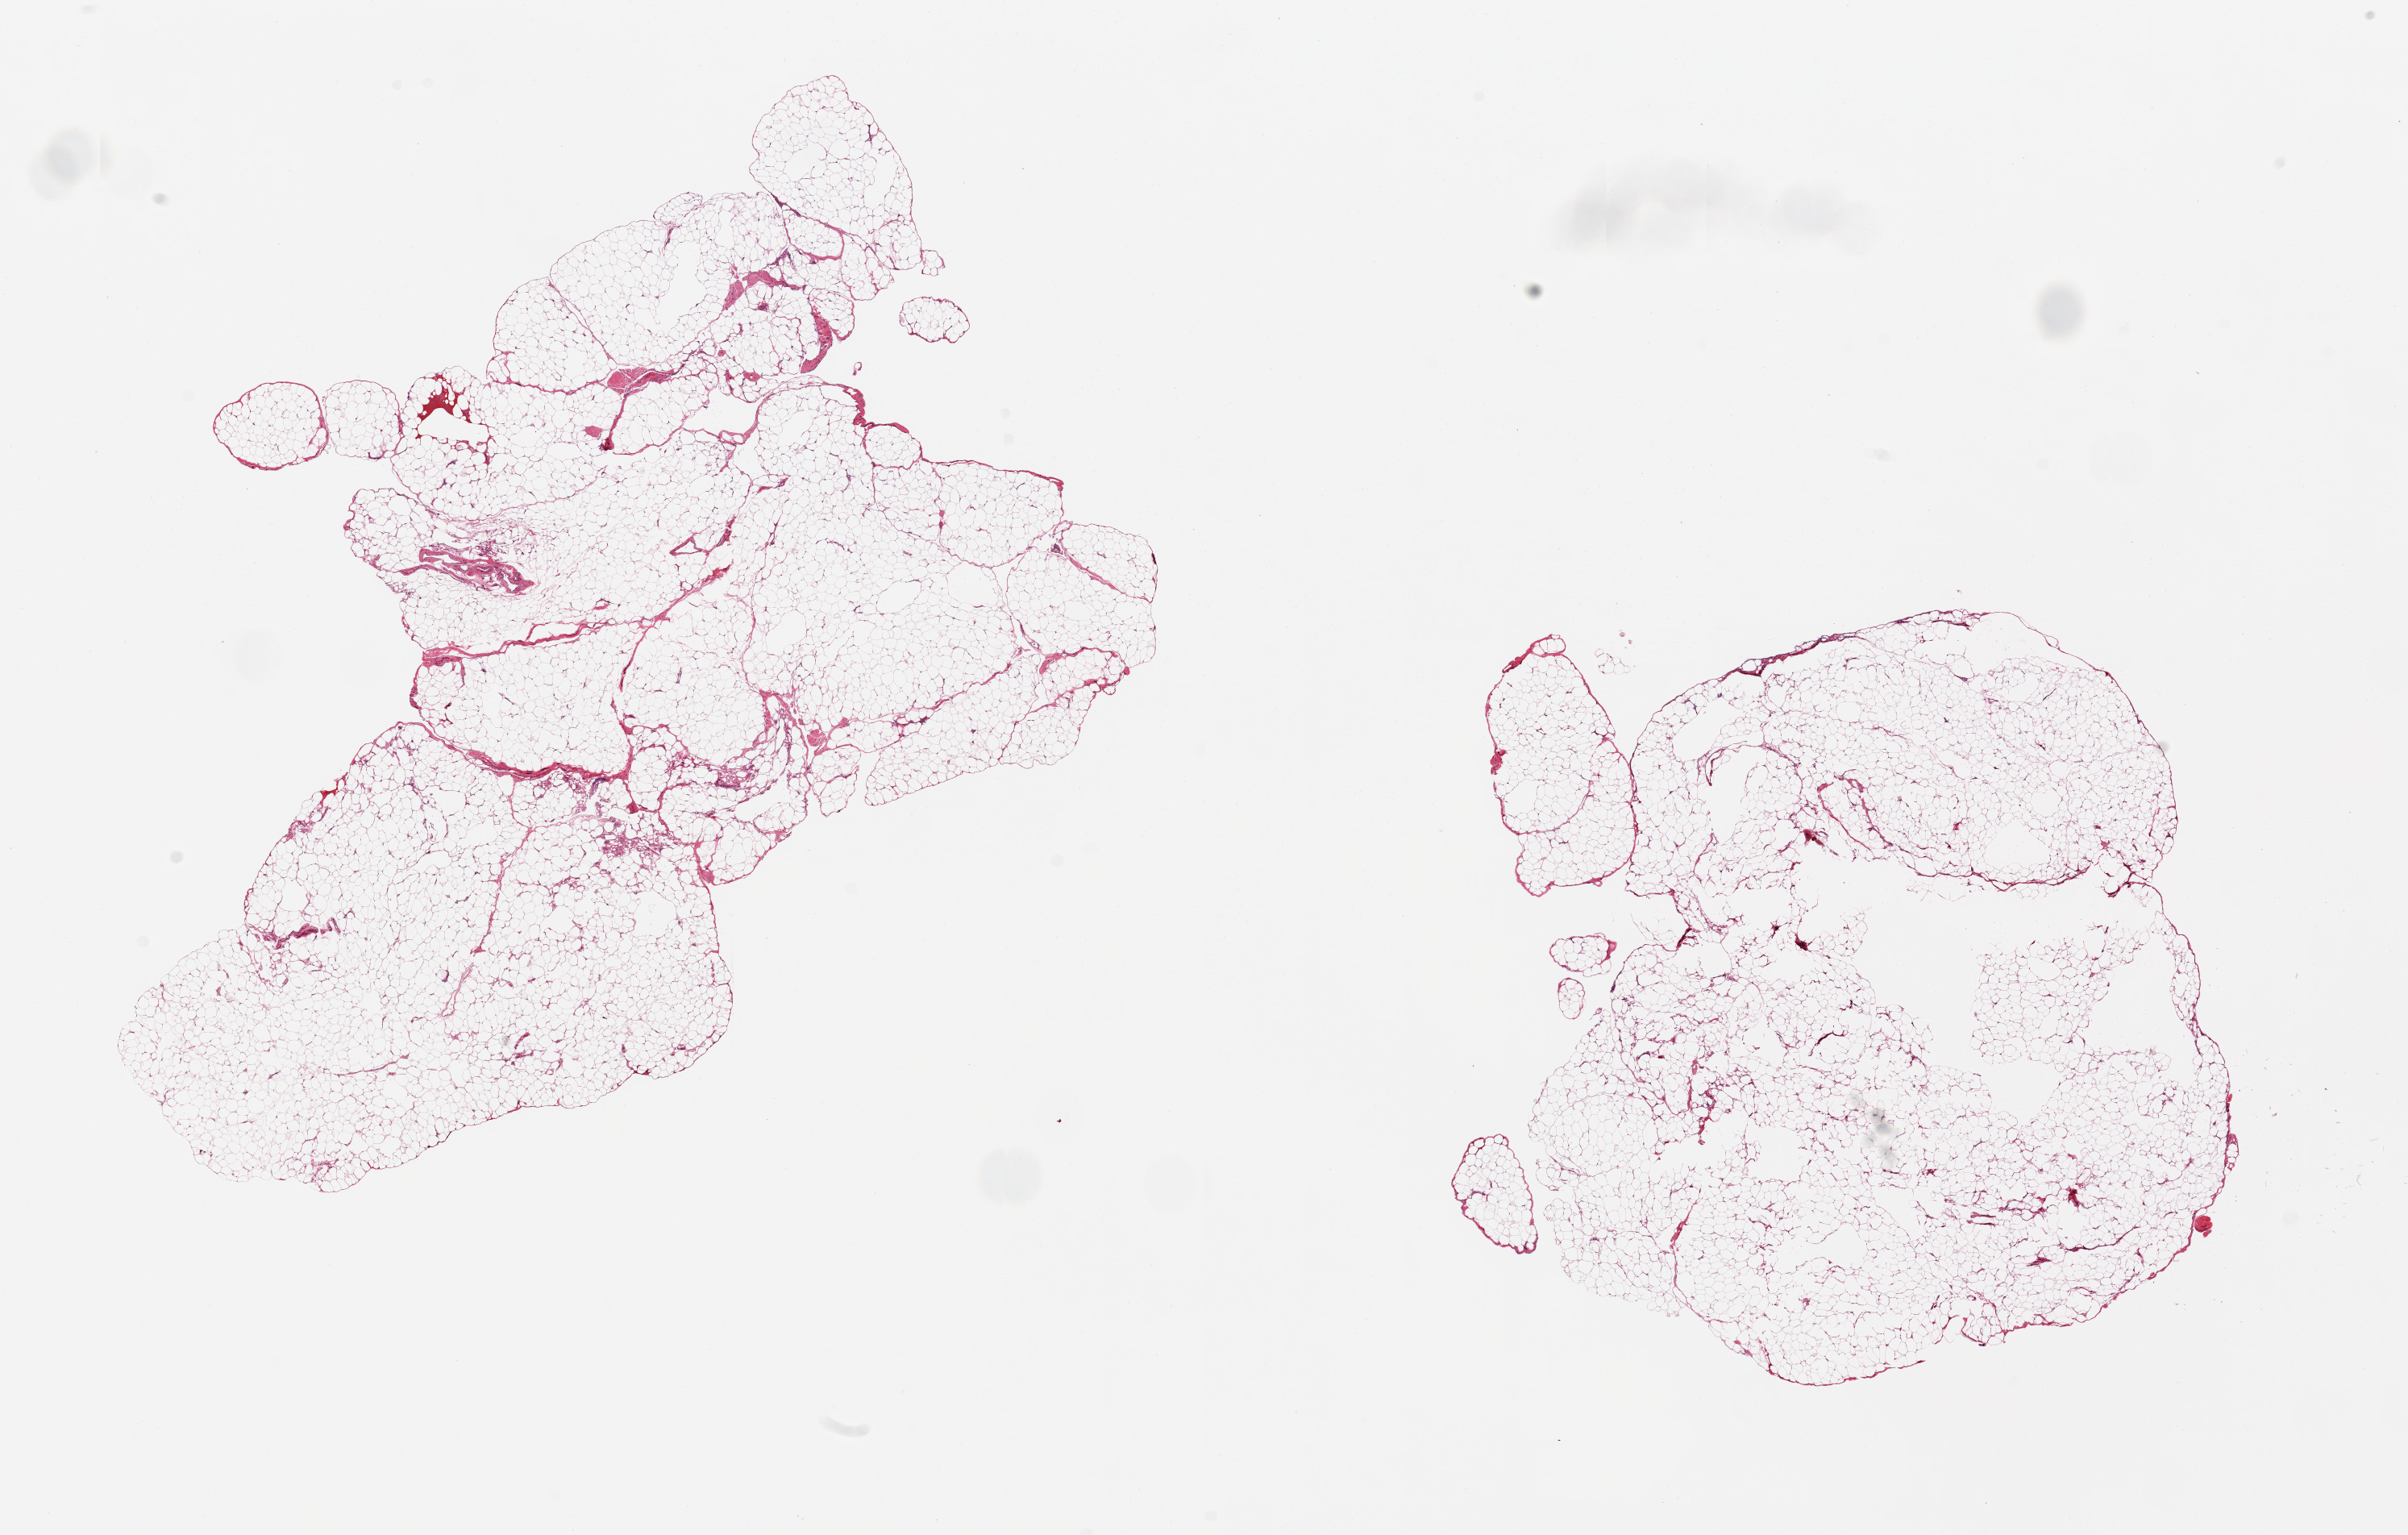
Digitized haematoxylin and eosin-stained section, a low-resolution overview of the entire scanned area, about 23.6 x 15.1 mm; PAXgene-fixed paraffin-embedded (PFPE) section; target tissue: omentum; donor tissue sample. Donor: male.
Reviewer comment on this tissue sample: 2 pieces, minimal vascular/fascial tissue.